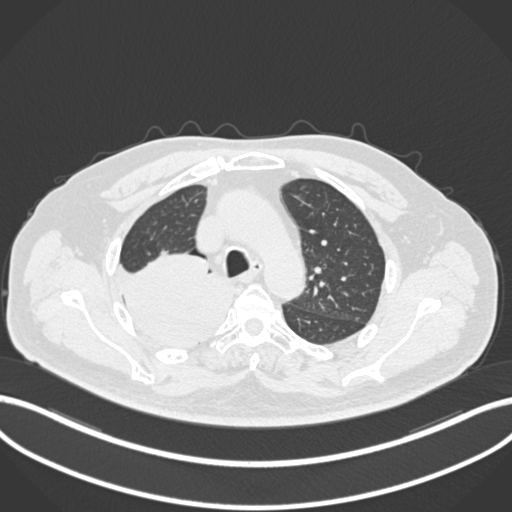
Chest CT, one axial slice. Slice 152 of 218 in the series (ordered by position). 120 kVp. Lung window (W 1500 / L -600 HU). 1 mm slice thickness. 512 × 512 image matrix, field of view 400 × 400 mm. Male patient, age 68 years. Case-level facts recorded for this patient, not image findings: clinical TNM (as recorded): T2a N0 M0.
Annotated regions visible in this slice (bounding box drawn by a radiologist):
- lung tumour (recorded histology: adenocarcinoma): bounding box [x1, y1, x2, y2] px = [116, 250, 239, 350]